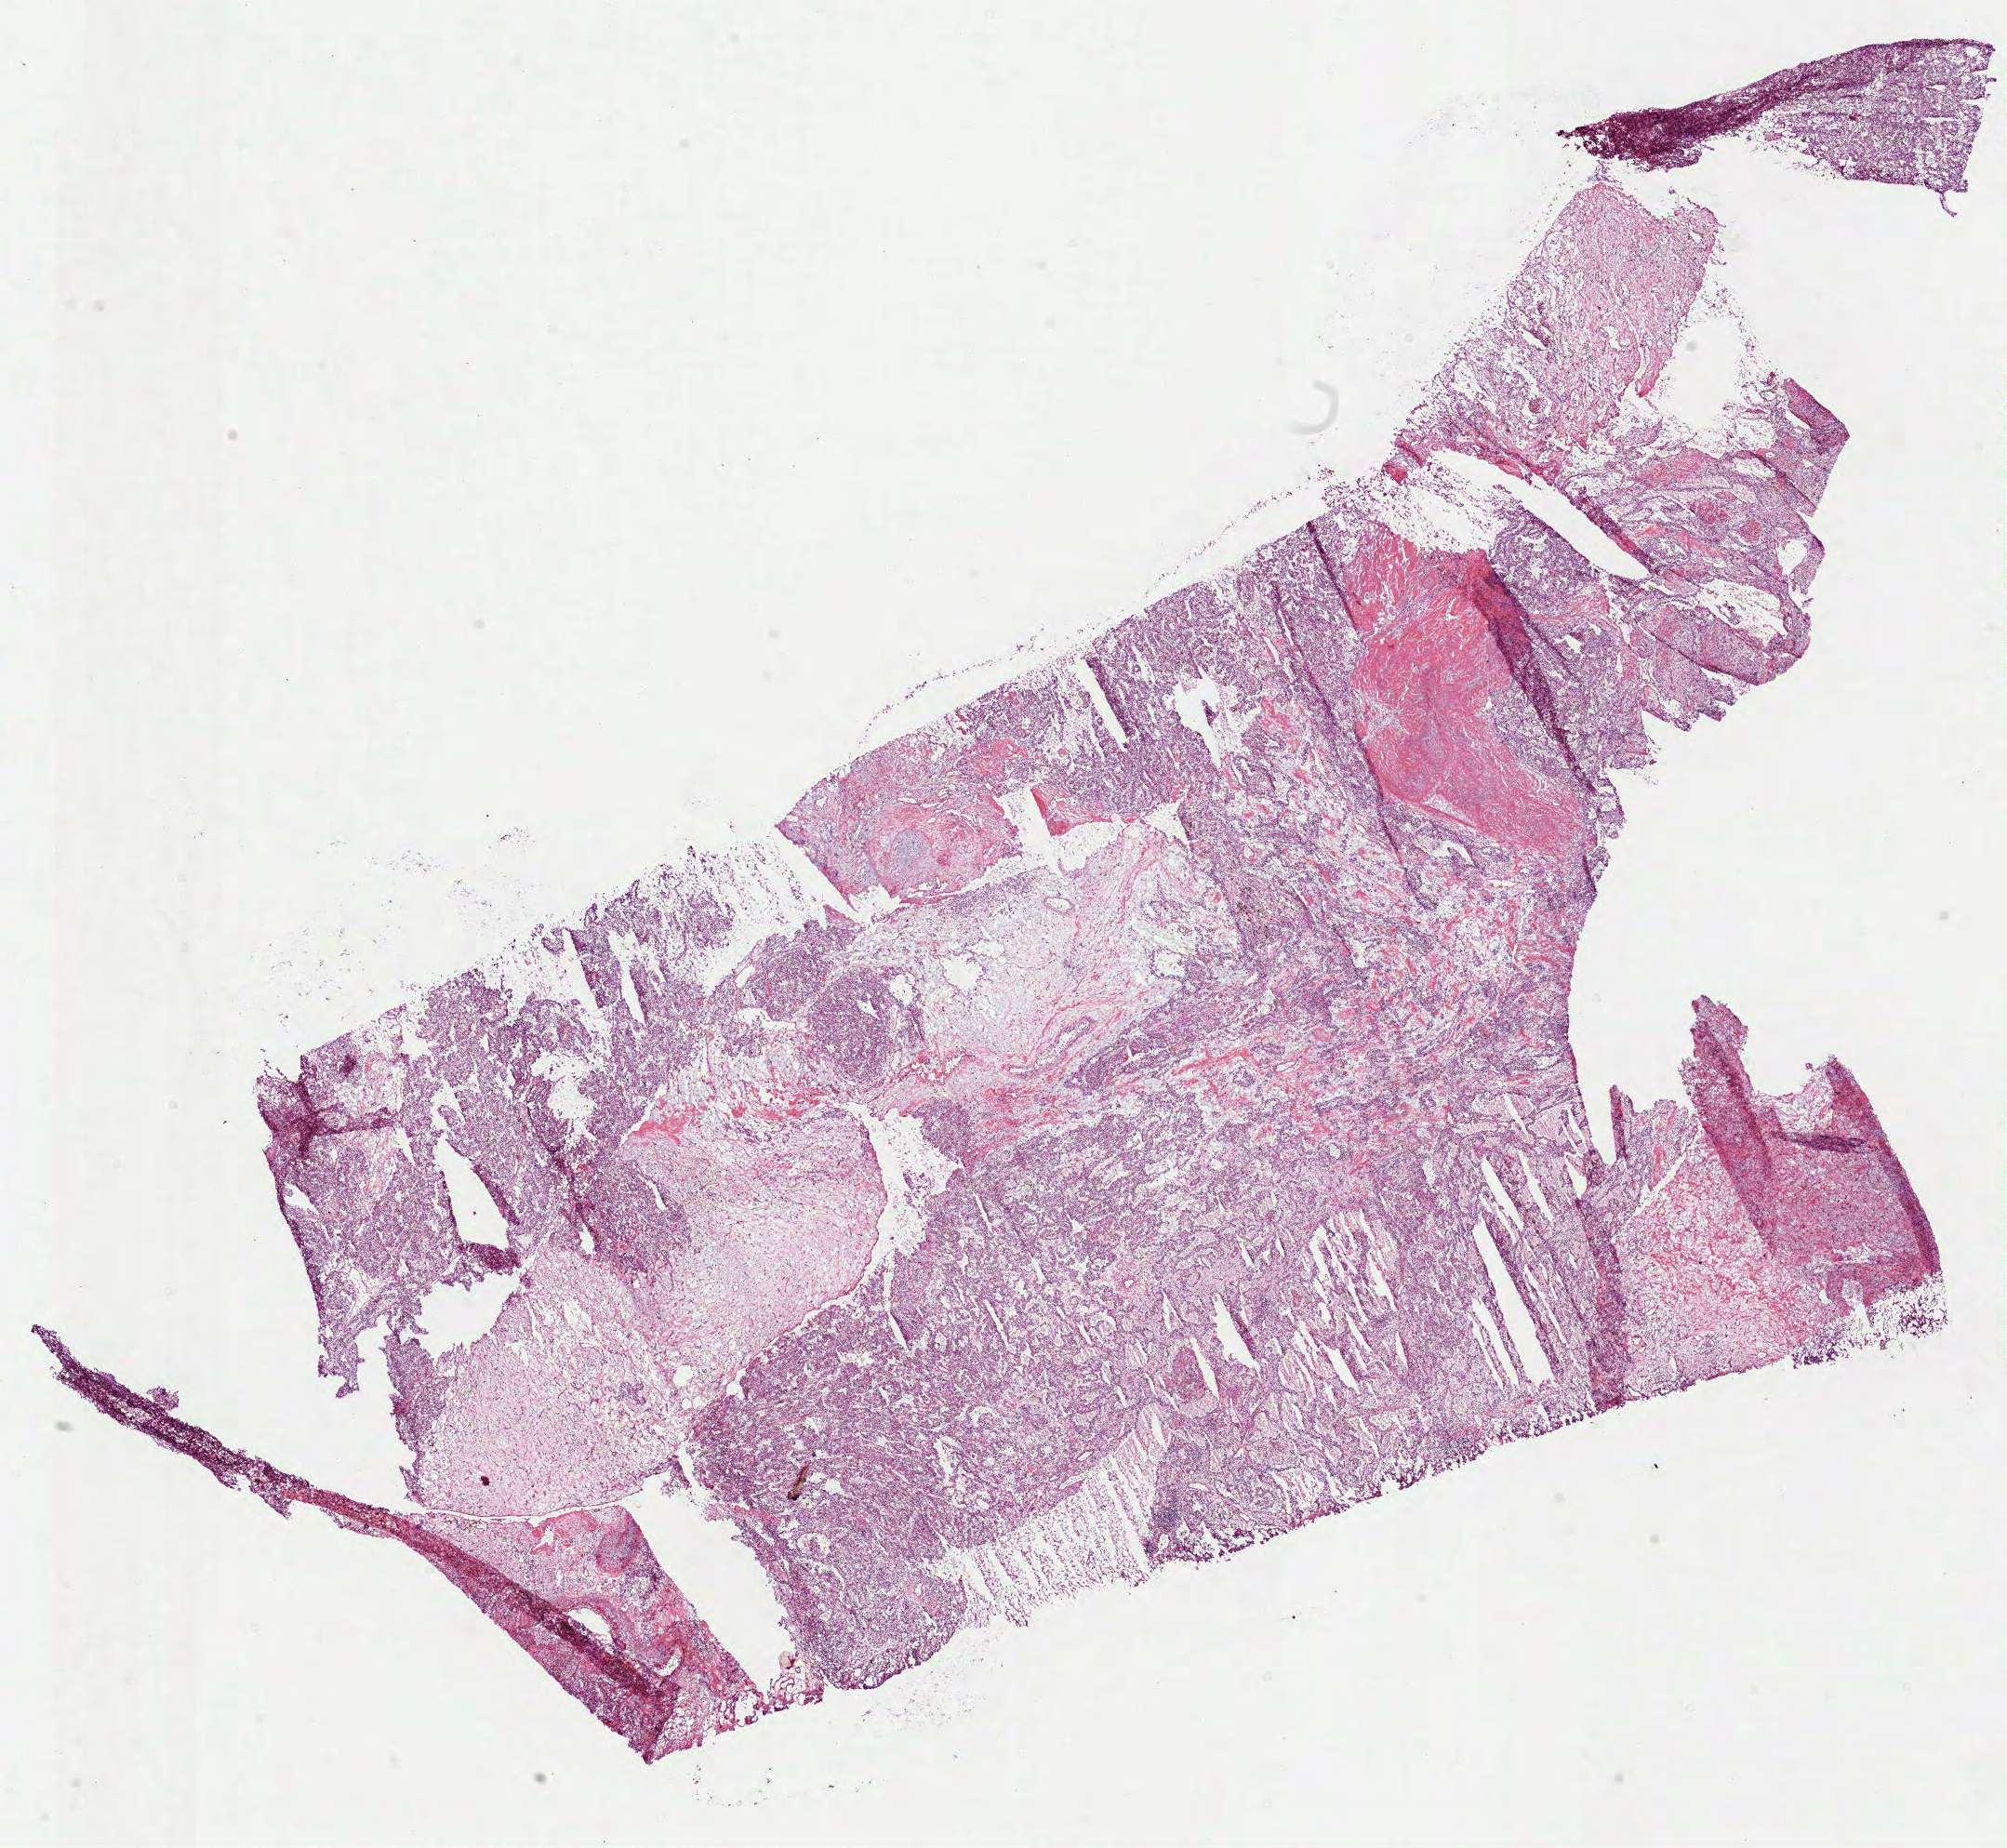
Whole-slide histology image, H&E — a low-resolution overview of the entire scanned area, about 17.4 x 16.0 mm; frozen section from the bottom of the tissue portion; kidney, primary tumour sample. Male patient; age at initial diagnosis 54 years. Histologic grade: G3 (poorly differentiated). Pathologist review of this section (percent, as recorded): tumour cells 85%, tumour nuclei 80%, normal cells 0%, stromal cells 15%, necrosis 0%.
• AJCC pathologic stage: I (7th edition)
• histologic diagnosis: Clear cell adenocarcinoma, NOS